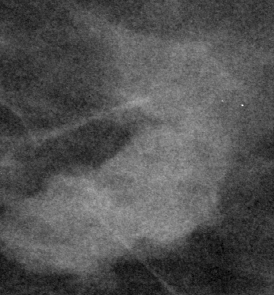
Crop from a digitized film mammogram around one marked abnormality, left breast, CC view, BI-RADS breast density category 2 (scale 1–4).
- Marked abnormality: mass, shape lobulated, margins circumscribed / microlobulated; BI-RADS assessment category 4; pathology result (as recorded, not read from the image): benign.